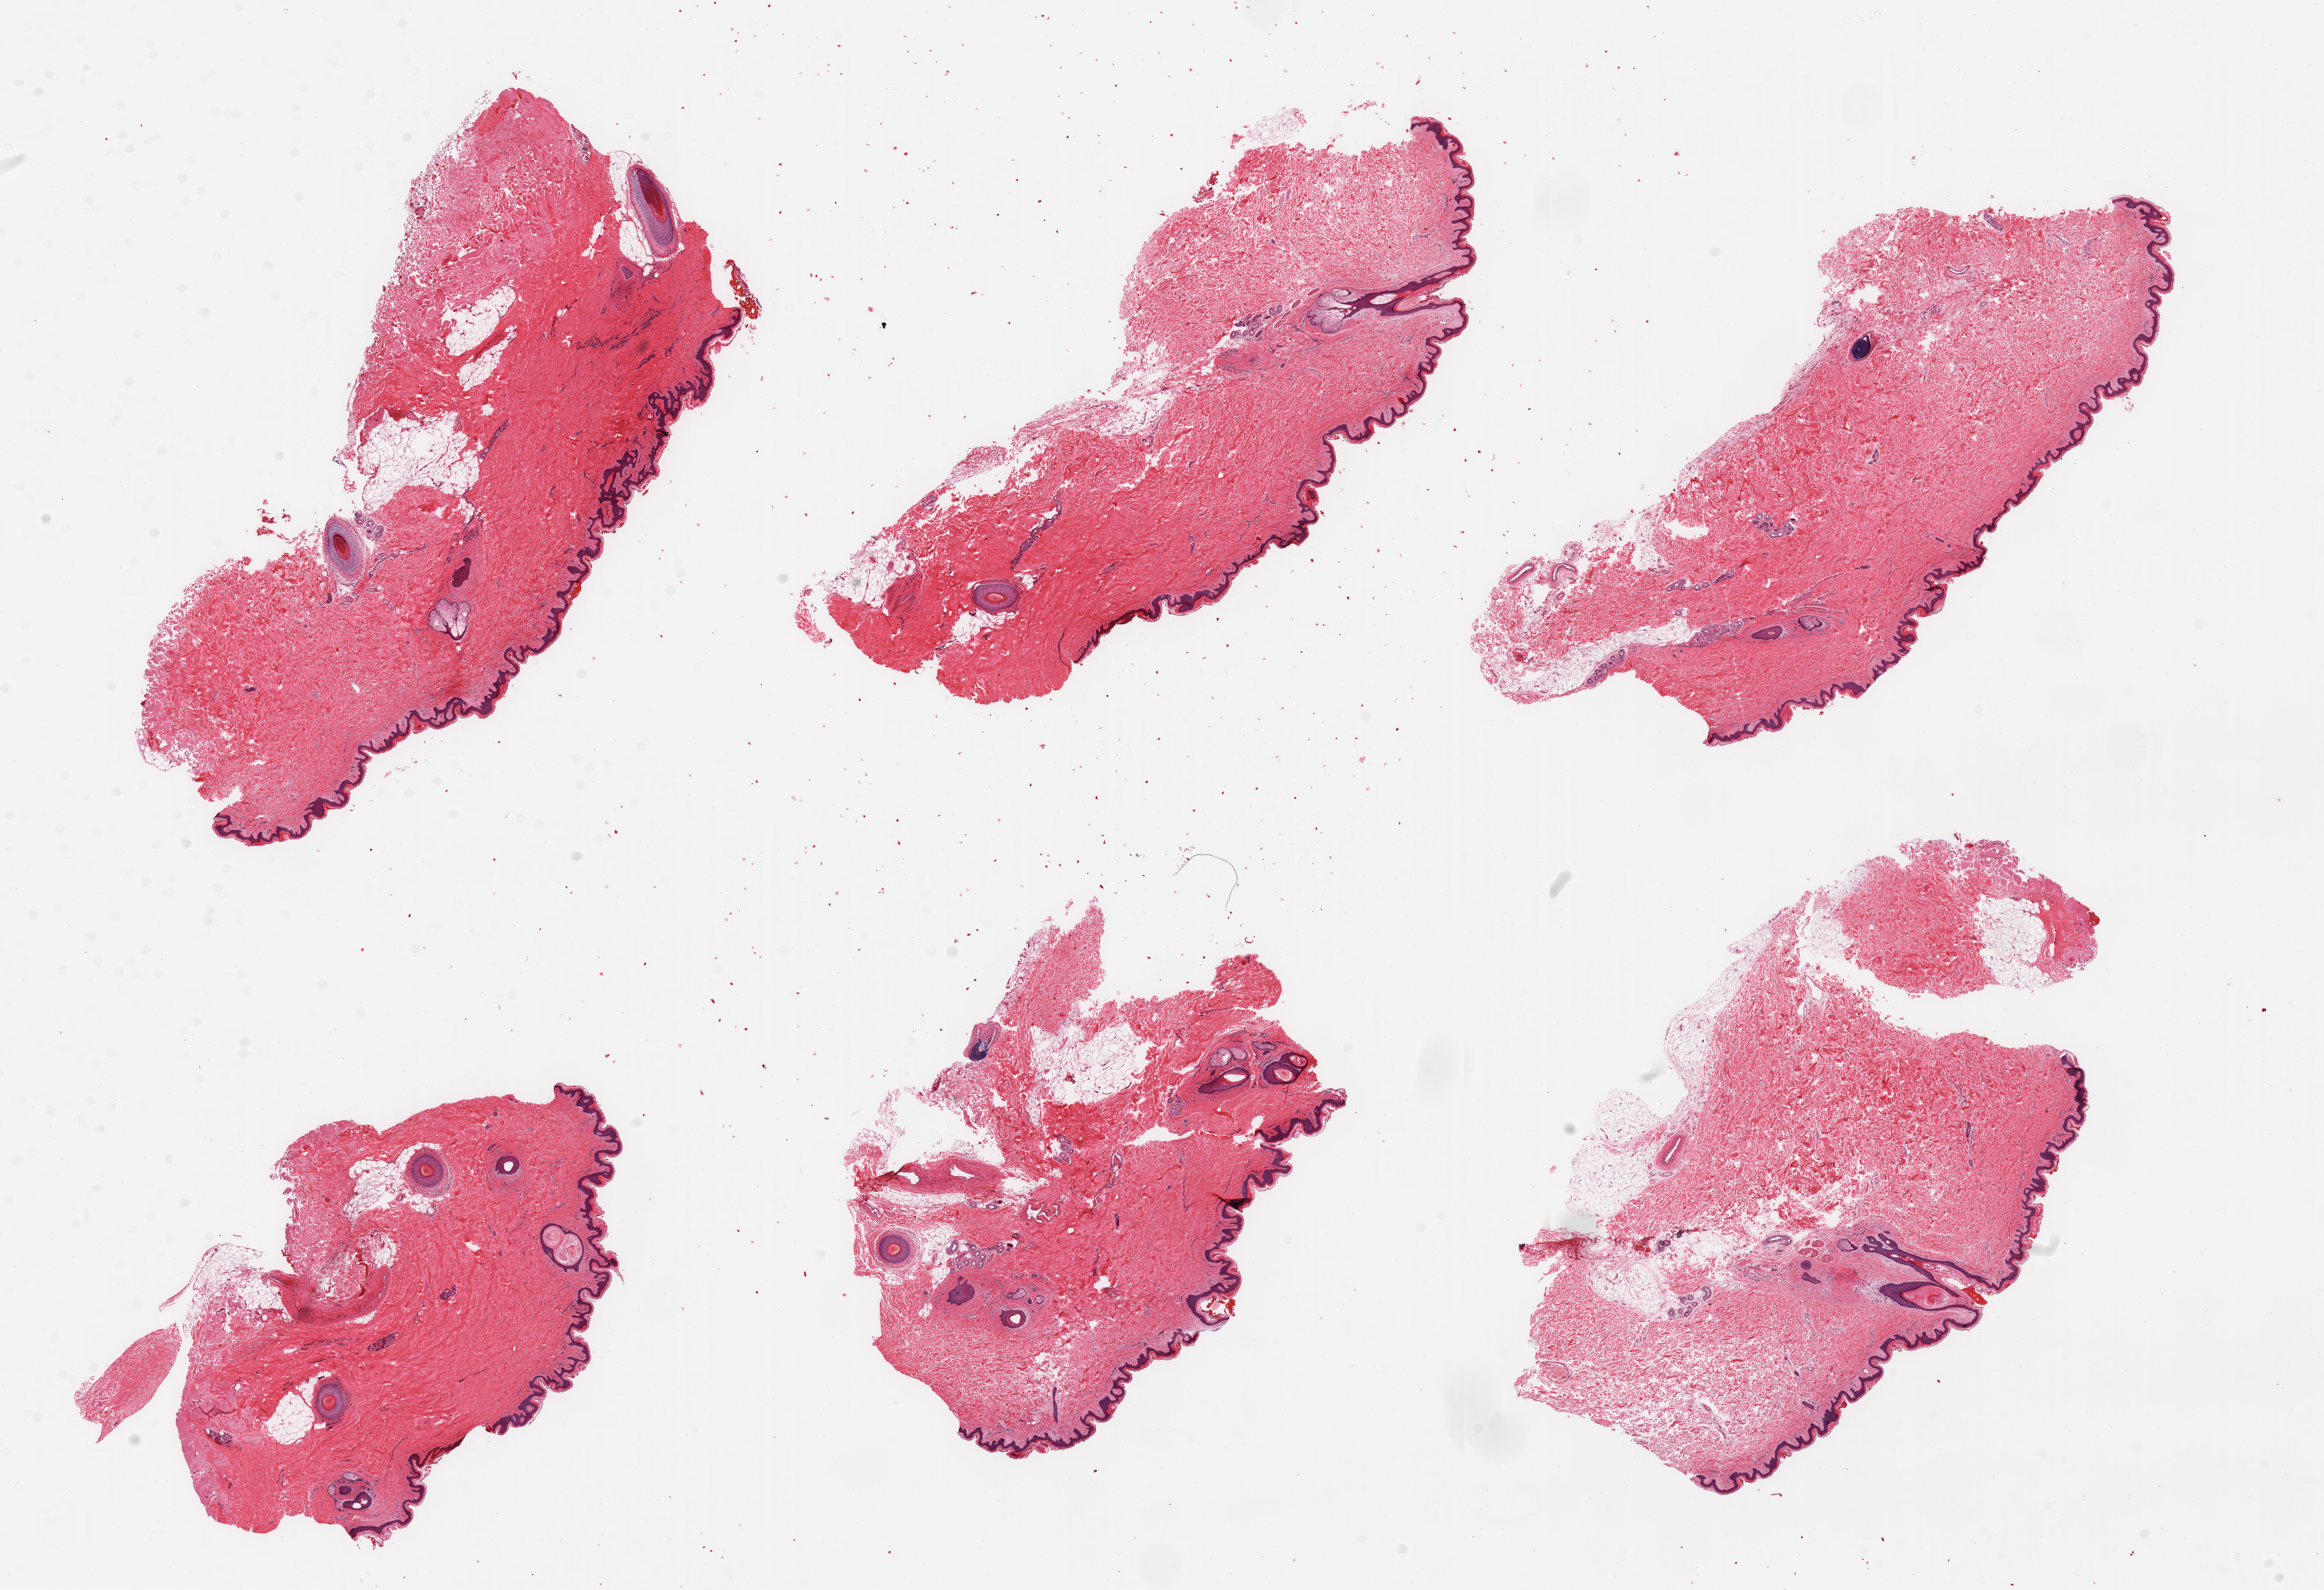
Whole-slide image, haematoxylin and eosin stain — a low-resolution overview of the entire scanned area, about 26.6 x 18.2 mm. PAXgene-fixed paraffin-embedded (PFPE) section. Section of skin of suprapubic region (target tissue). Donor tissue sample. Male donor.
Review note (as recorded): 6 pieces; includes up to ~10% fat, hair bearing skin.